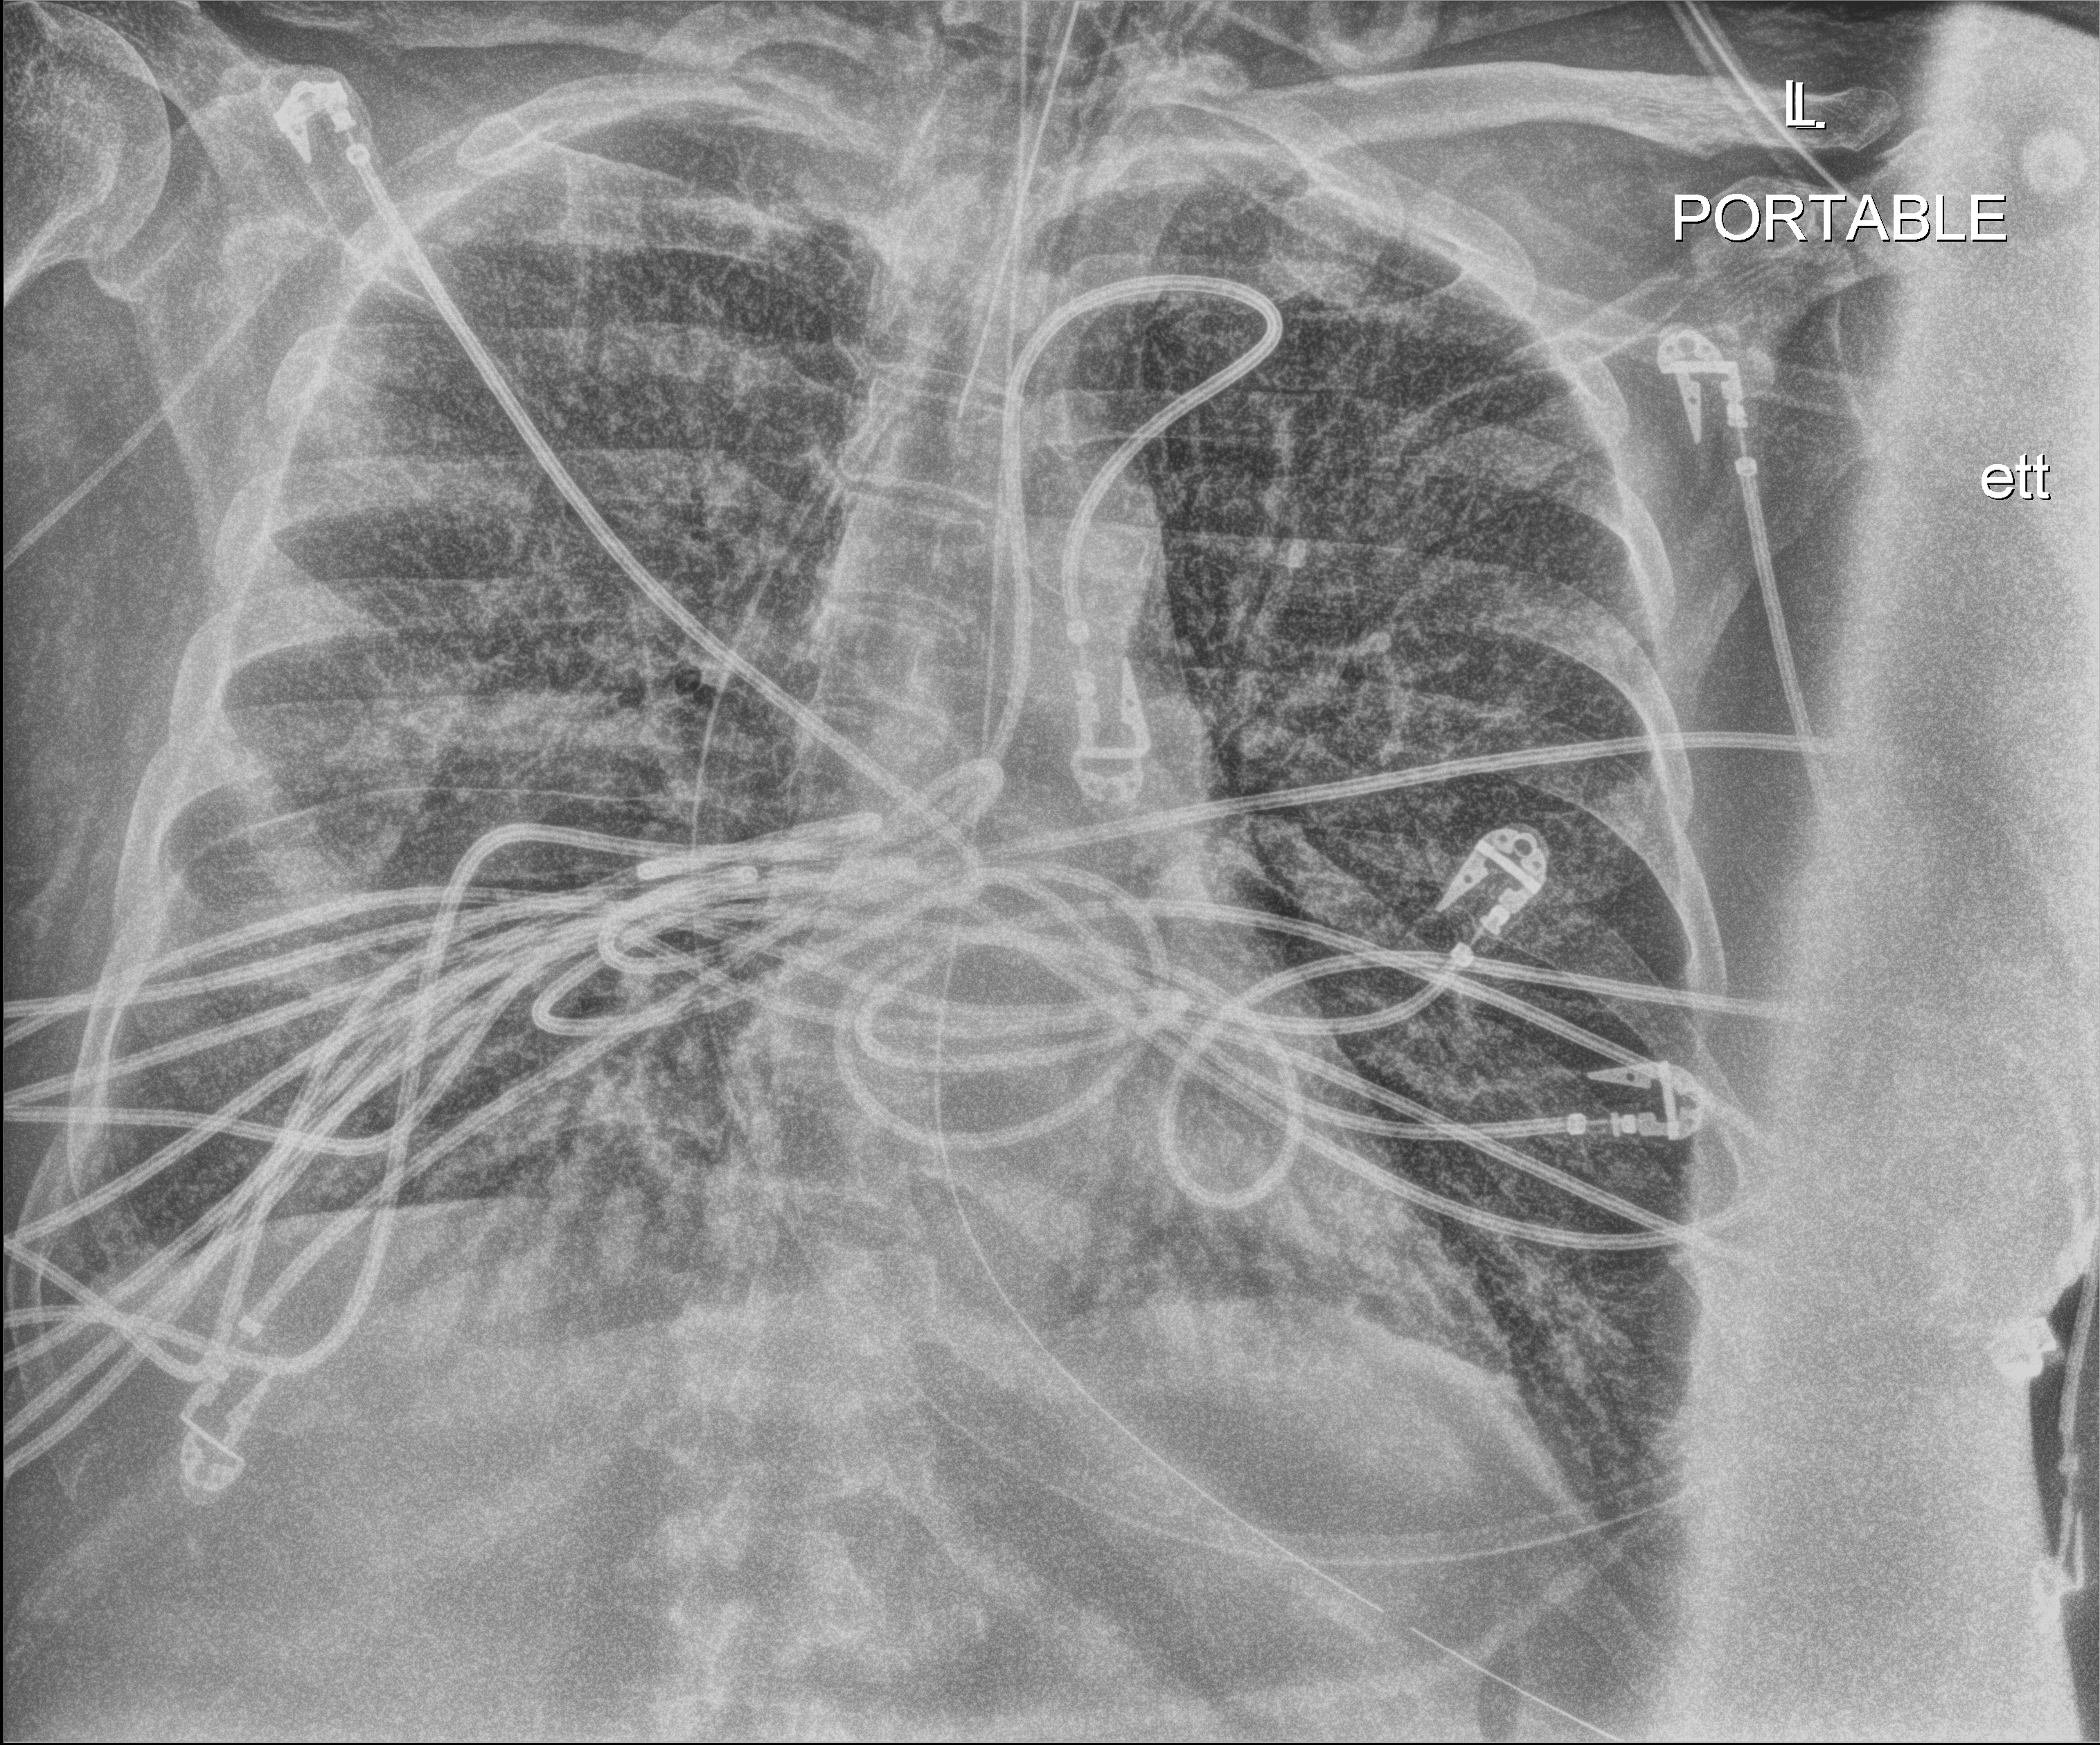
Chest radiograph, anteroposterior (AP) projection. Male patient hospitalised with COVID-19, age 60–74 years.
From the hospital-stay record, not from the radiograph (when in the stay this image was taken is not recorded): mechanically ventilated during this hospital stay: yes.